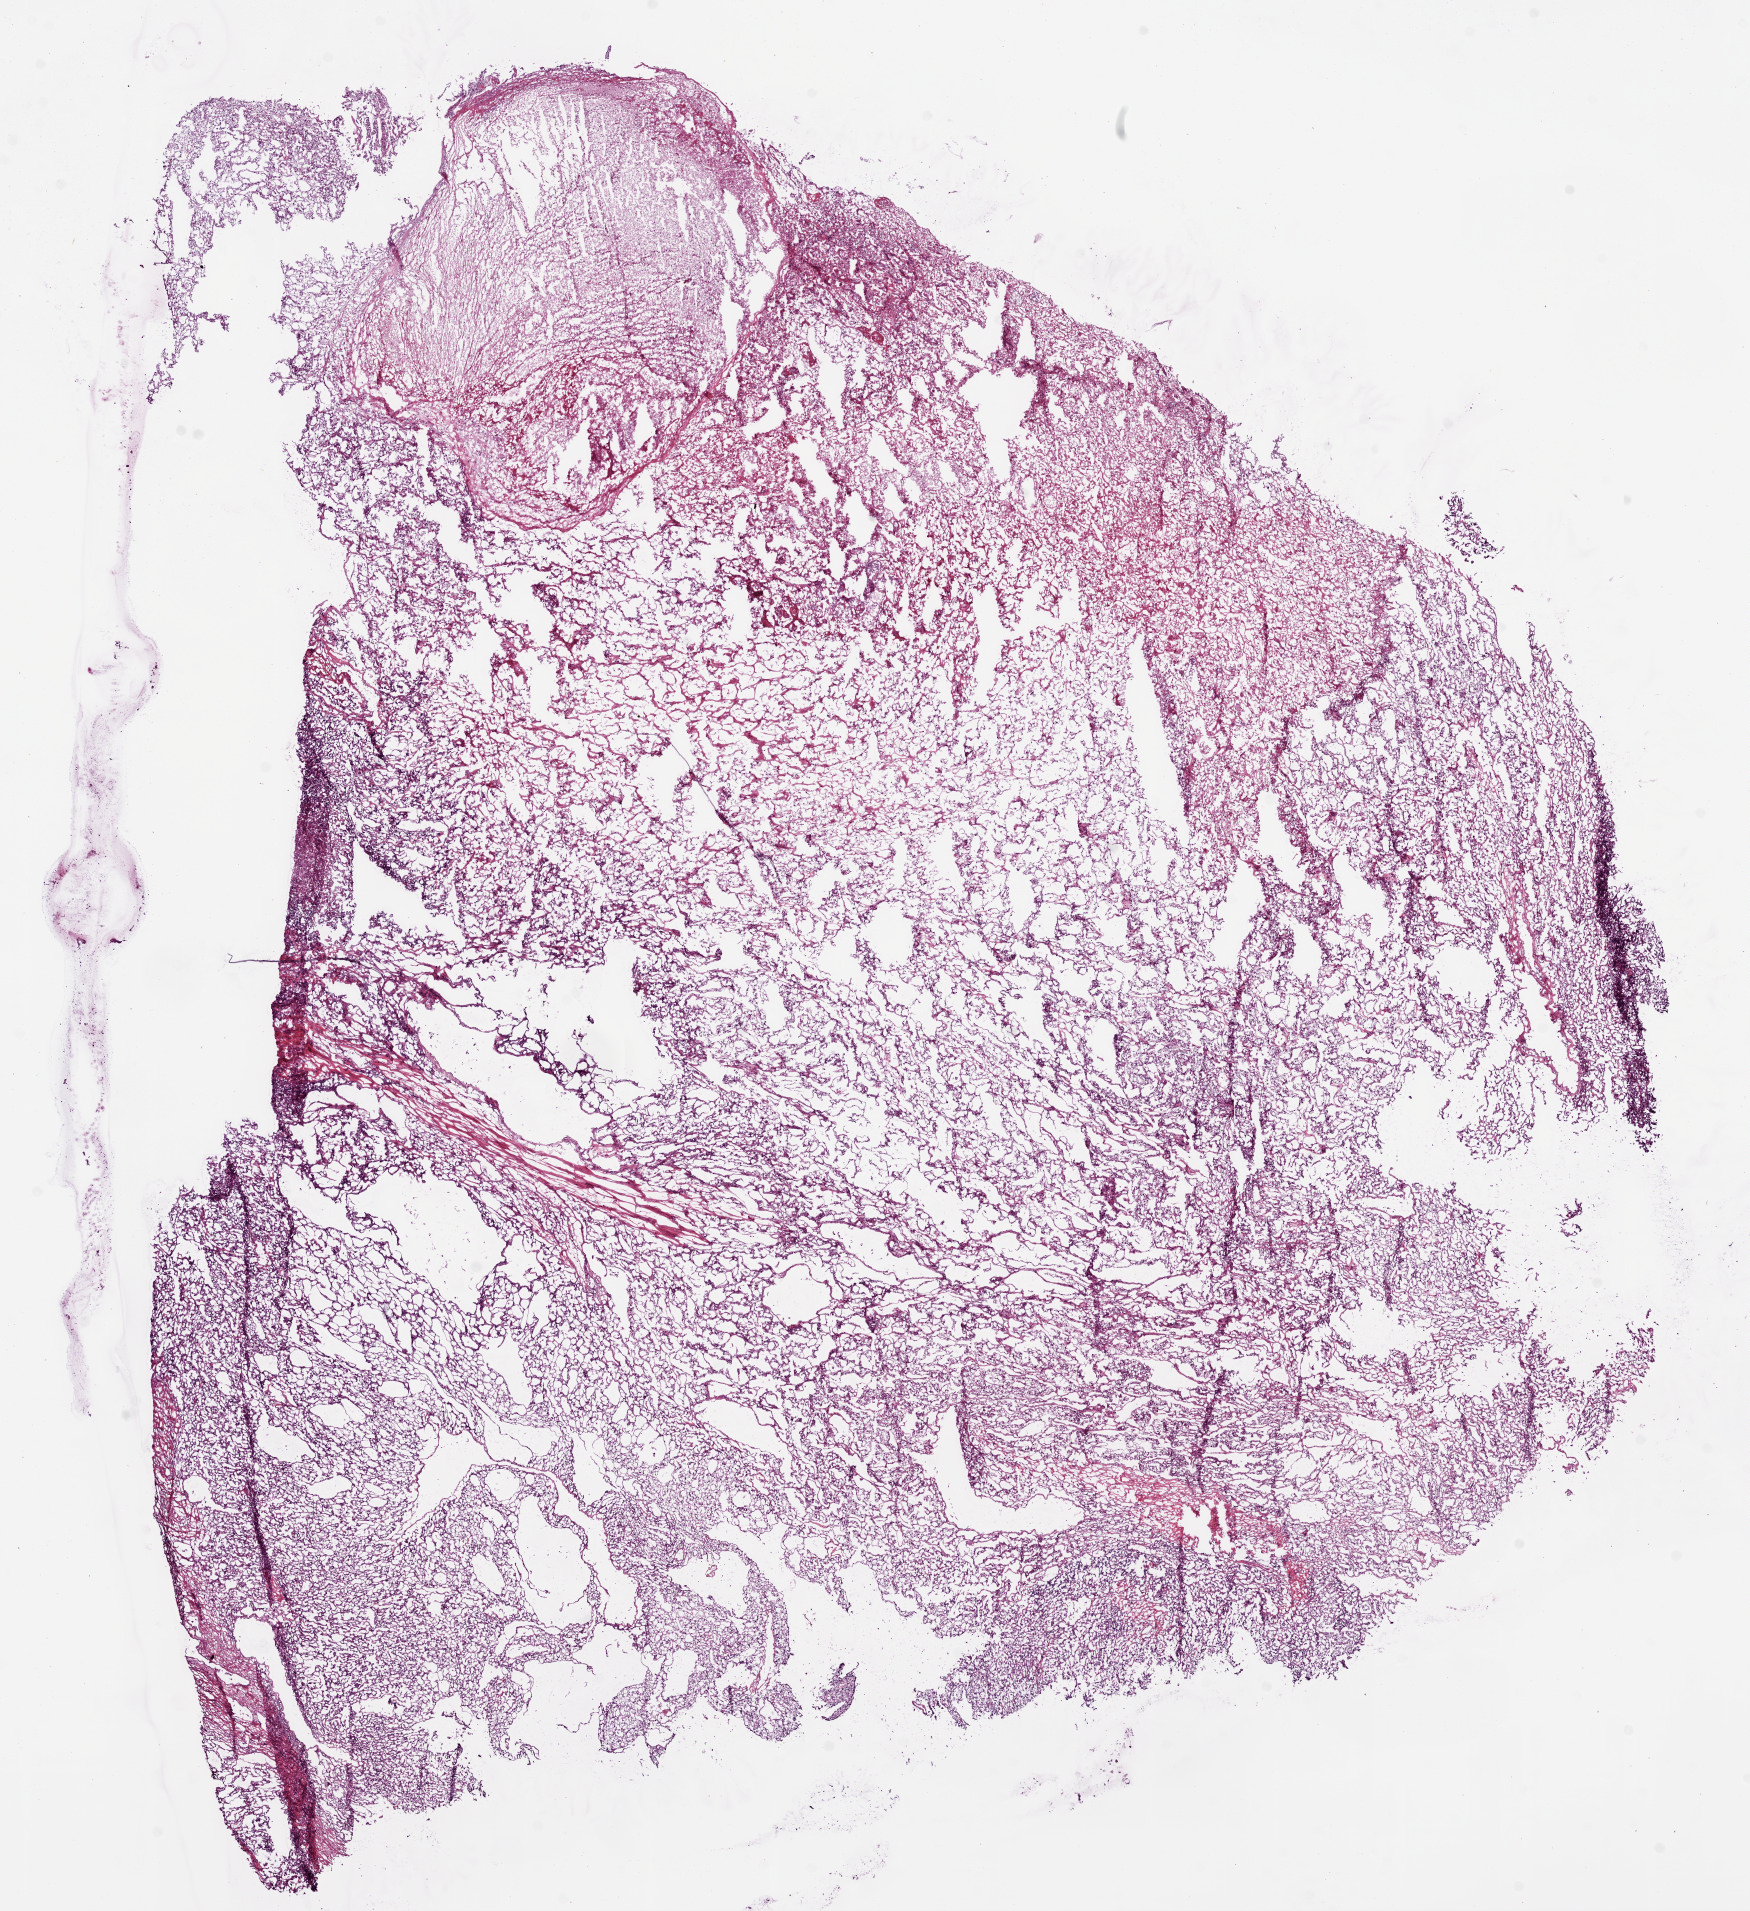
Digitized Hematoxylin and eosin (H&E) stained tissue section (whole slide), shown as a low-resolution overview of the whole scanned area (about 14.0 x 15.3 mm, slide scanned at 20x), frozen section from the bottom of the tissue portion, primary tumour sample from the kidney. Female, age 68 years at initial diagnosis. Histologic grade: G3 (poorly differentiated). Slide review estimates, as recorded: tumour cells 87%, tumour nuclei 85%, normal cells 0%, stromal cells 10%, necrosis 3%.
Histologic diagnosis: Clear cell adenocarcinoma, NOS. AJCC pathologic stage: III. Lymph nodes positive (case pathology): 0 of 1 examined.